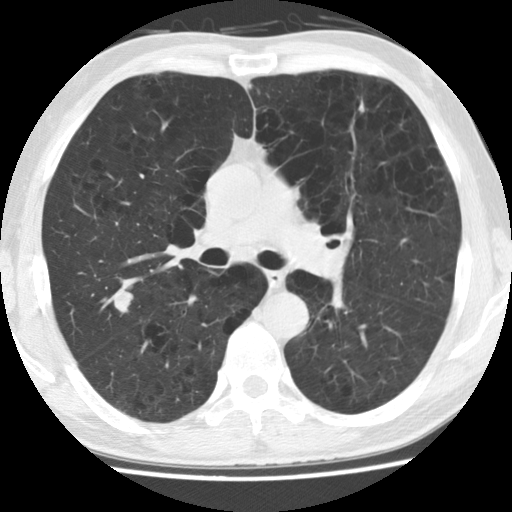
Chest CT (low-dose screening protocol), one axial image; baseline annual screen; lung window (W 1500 / L -600 HU); standard (soft-tissue) reconstruction kernel (STANDARD); slice 68 of 158 in the series. Male, age 62 years at enrolment. Current smoker at enrolment.
Lesion marked by an expert reader, box from (x=91, y=264) to (x=148, y=326) px. The screening reader recorded 2 non-calcified nodules or masses ≥4 mm on this exam; which of them this box marks is not recorded. Participant outcome: lung cancer diagnosed 288 days after this screen — oat cell carcinoma, right upper lobe, undifferentiated (G4), stage IV (AJCC 6th edition), 30 mm at pathology.